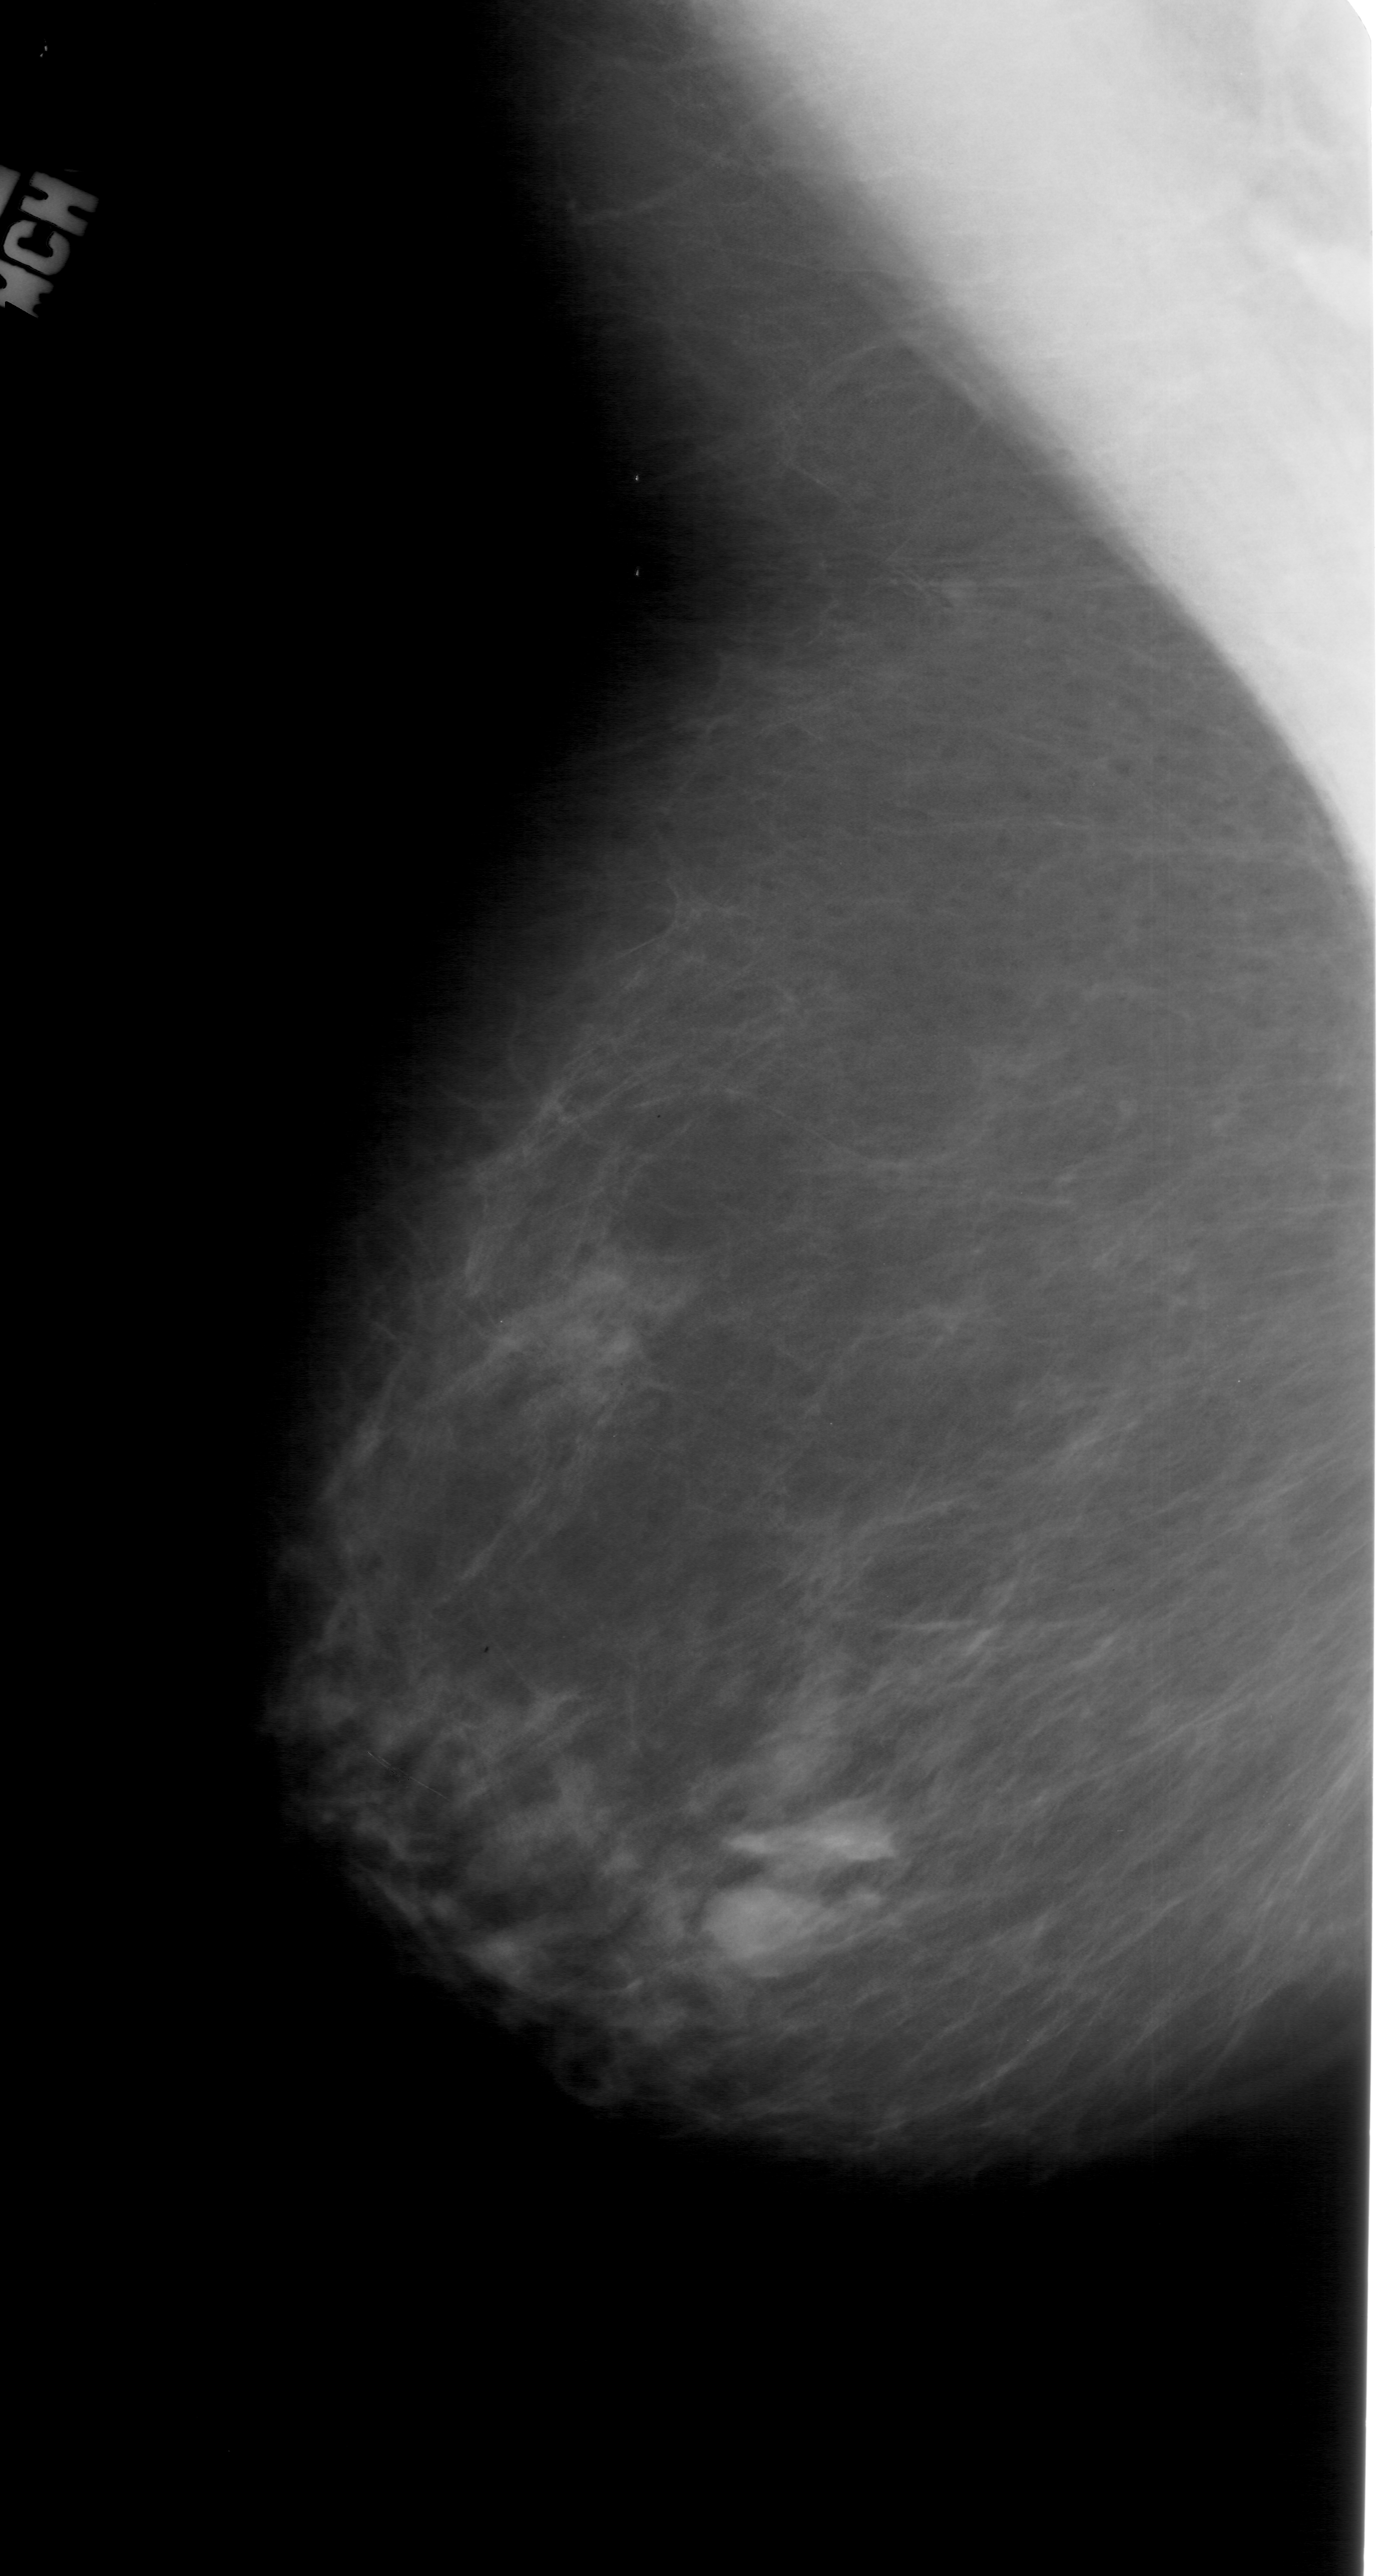
Digitized screen-film mammogram. Left breast. Mediolateral oblique (MLO) view. BI-RADS breast density category 2 (scale 1–4). 1382 × 2576 image matrix.
Expert-marked regions of interest on this image (one box per marked abnormality):
- mass, shape lobulated, margins ill defined; BI-RADS assessment category 4; subtlety rating 5 on a 1 (subtle) to 5 (obvious) scale; pathology (as recorded): benign: bounding box <702,1804,887,1981> (left, top, right, bottom; pixels)